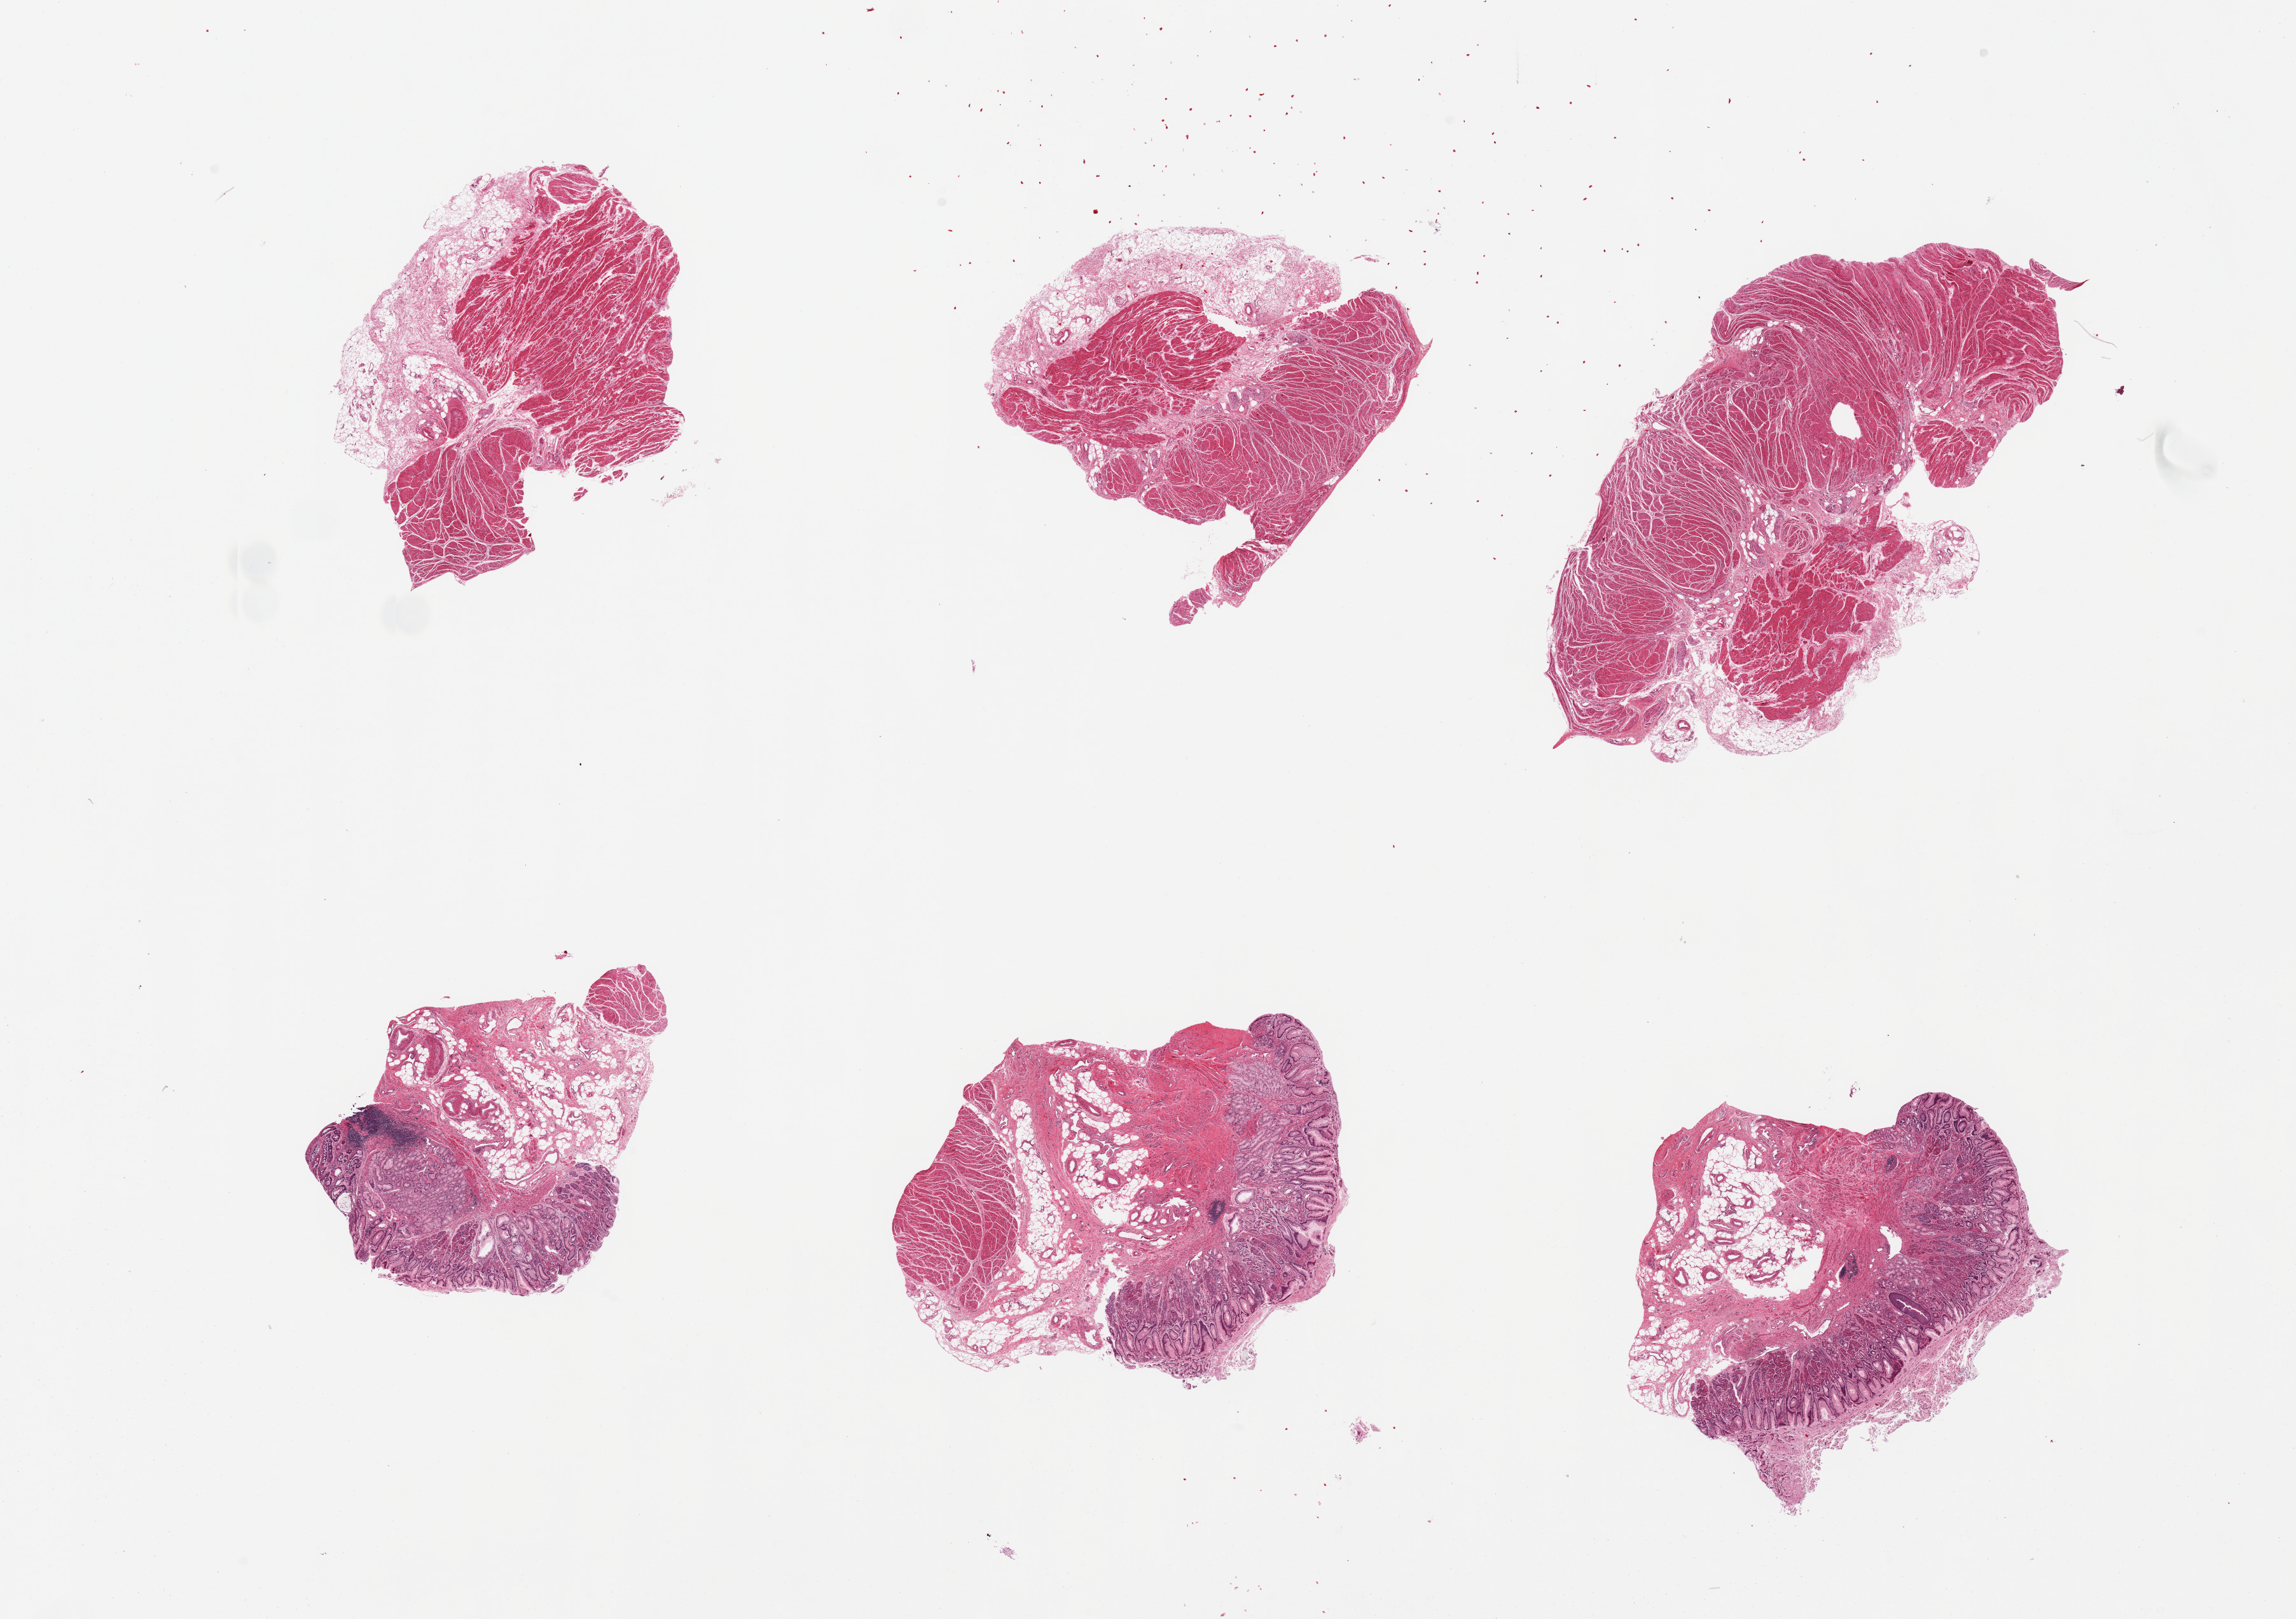
Digitized haematoxylin and eosin-stained section, low-resolution overview of the scanned area, about 28.5 x 20.1 mm; PAXgene-fixed, paraffin-embedded tissue; target tissue: gastroesophageal junction; tissue donor sample. Donor: male.
Review note (as recorded): 6 pieces: 1 with no muscle (all mucosa), 1, 20% muscle; 1,10% muscle.